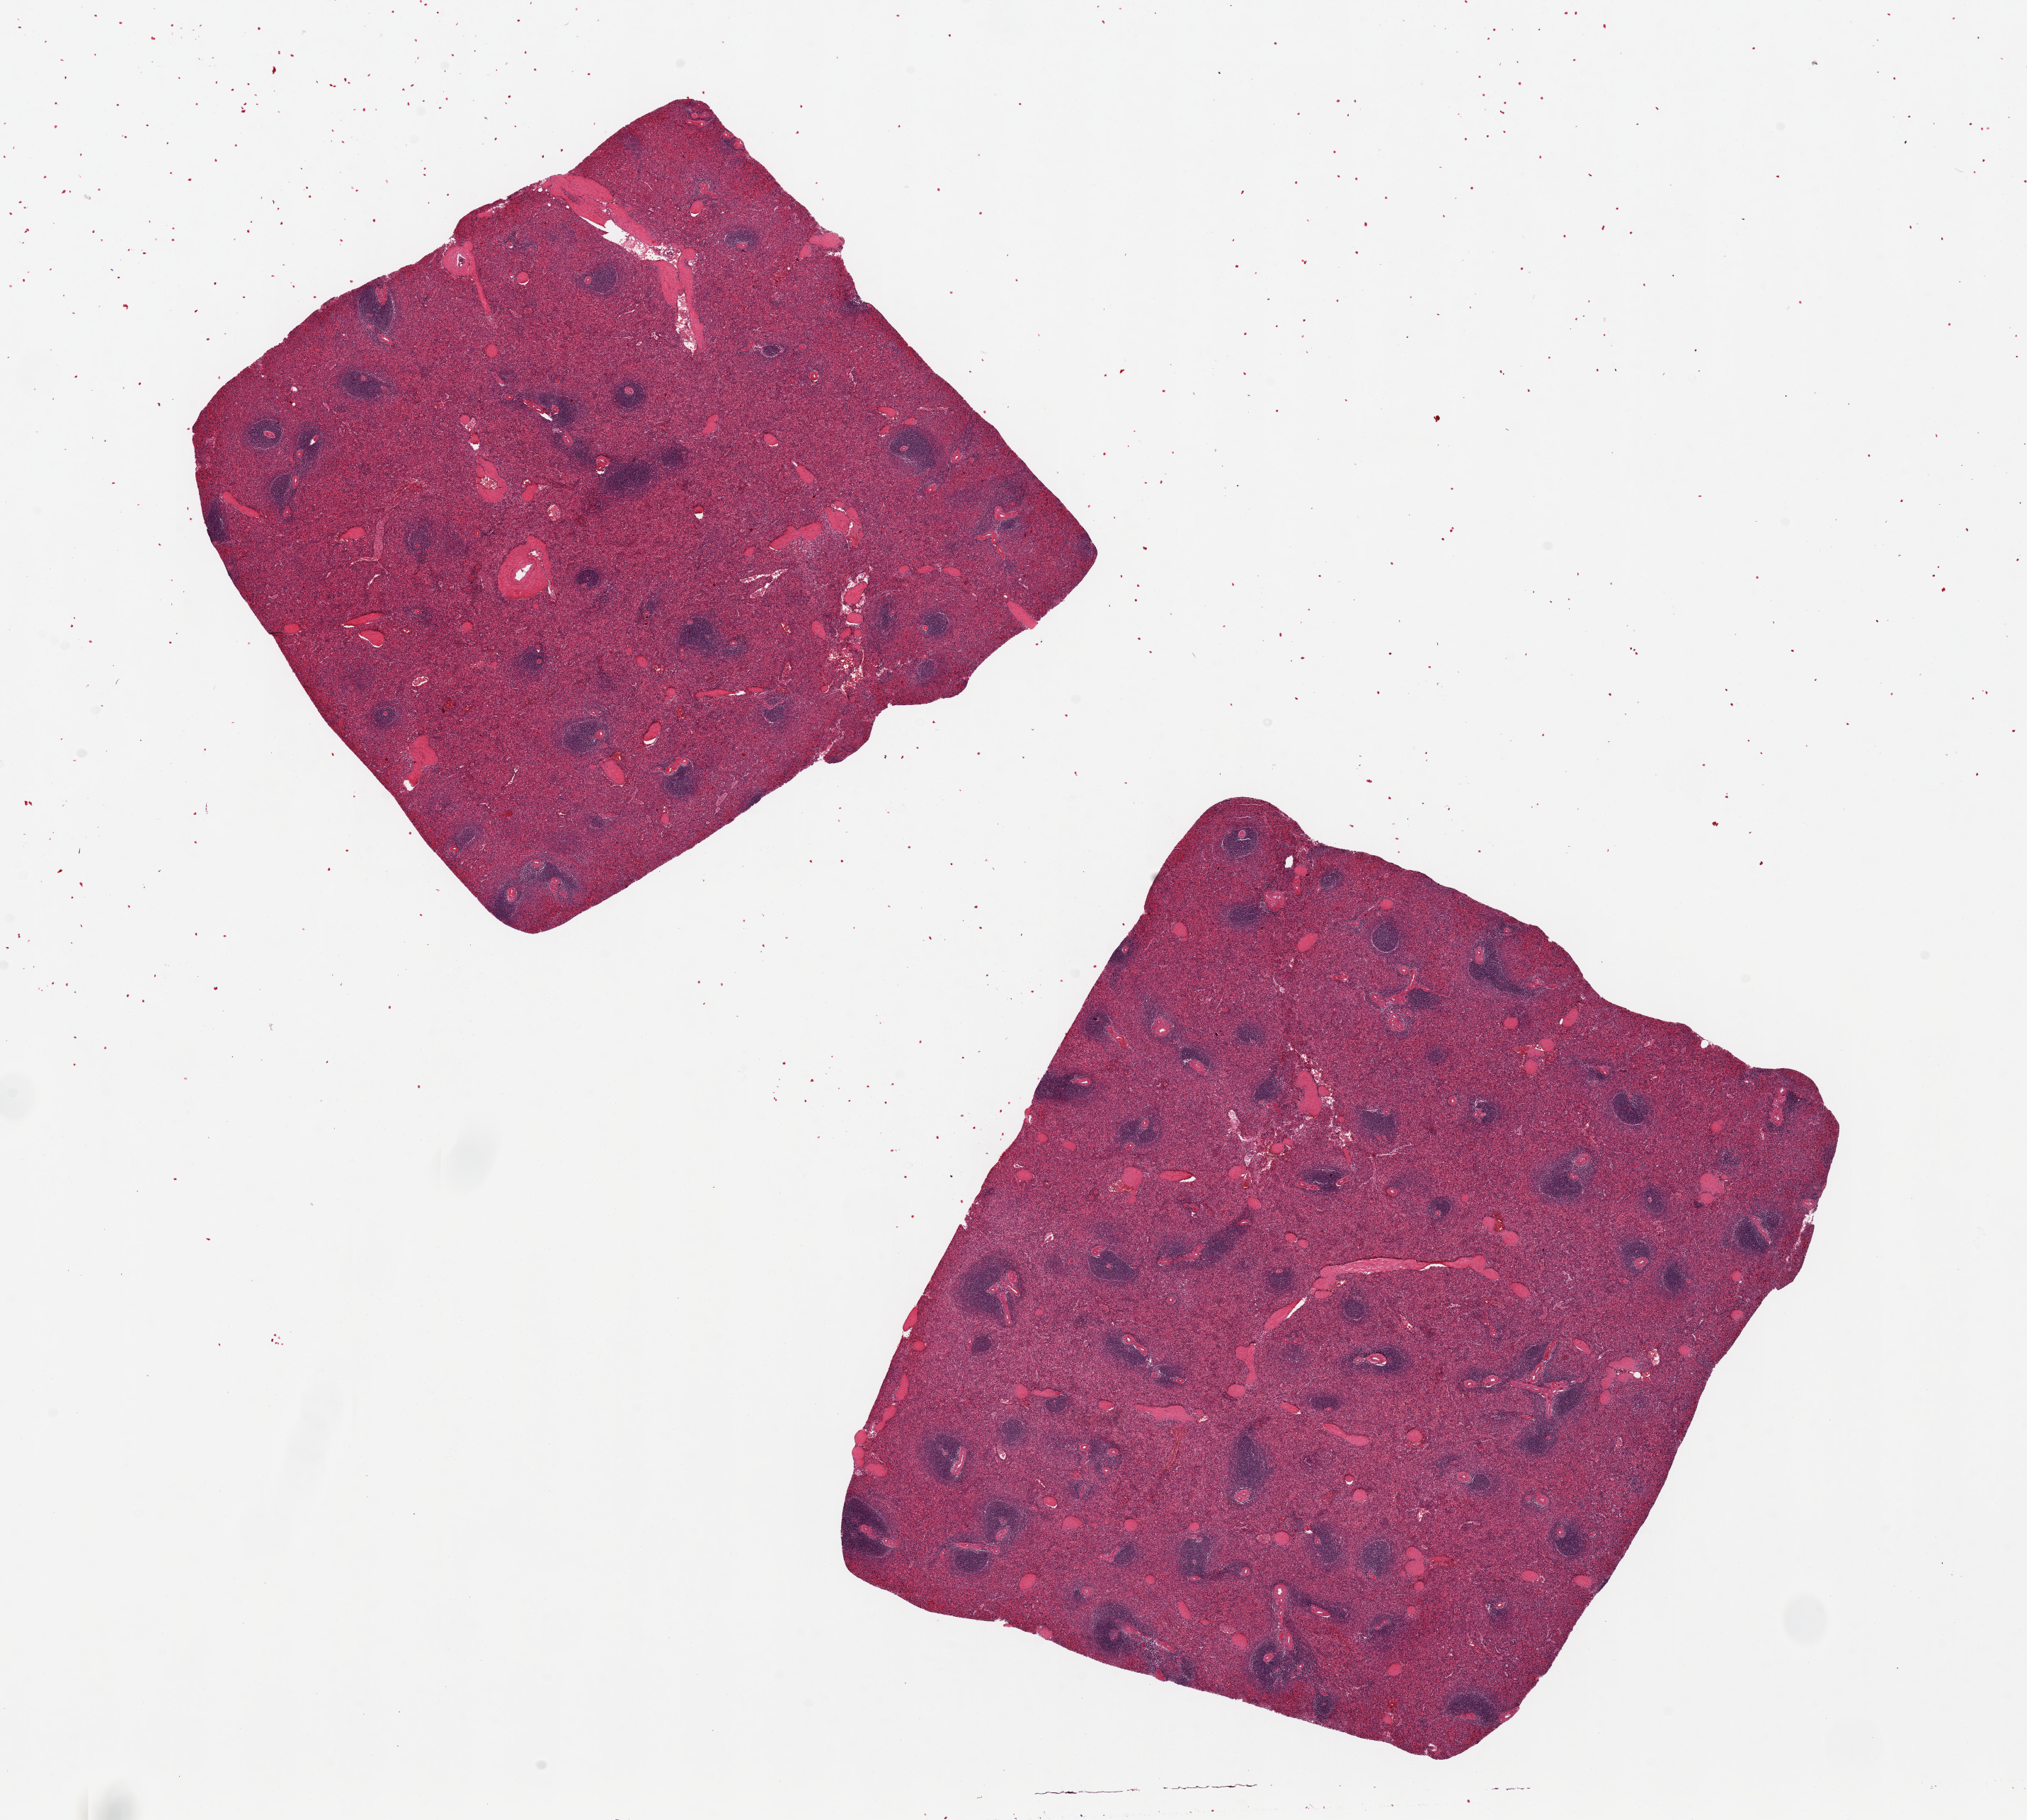
Whole-slide image, hematoxylin and eosin (H&E) stain, brightfield — low-resolution overview of the scanned area, about 22.6 x 20.3 mm (slide scanned at 20x); PAXgene-fixed, paraffin-embedded tissue; sampled site (target tissue): spleen; tissue donor sample. Donor sex: male.
Pathologist's review note for this sample: 2 pieces ~10x8mm.